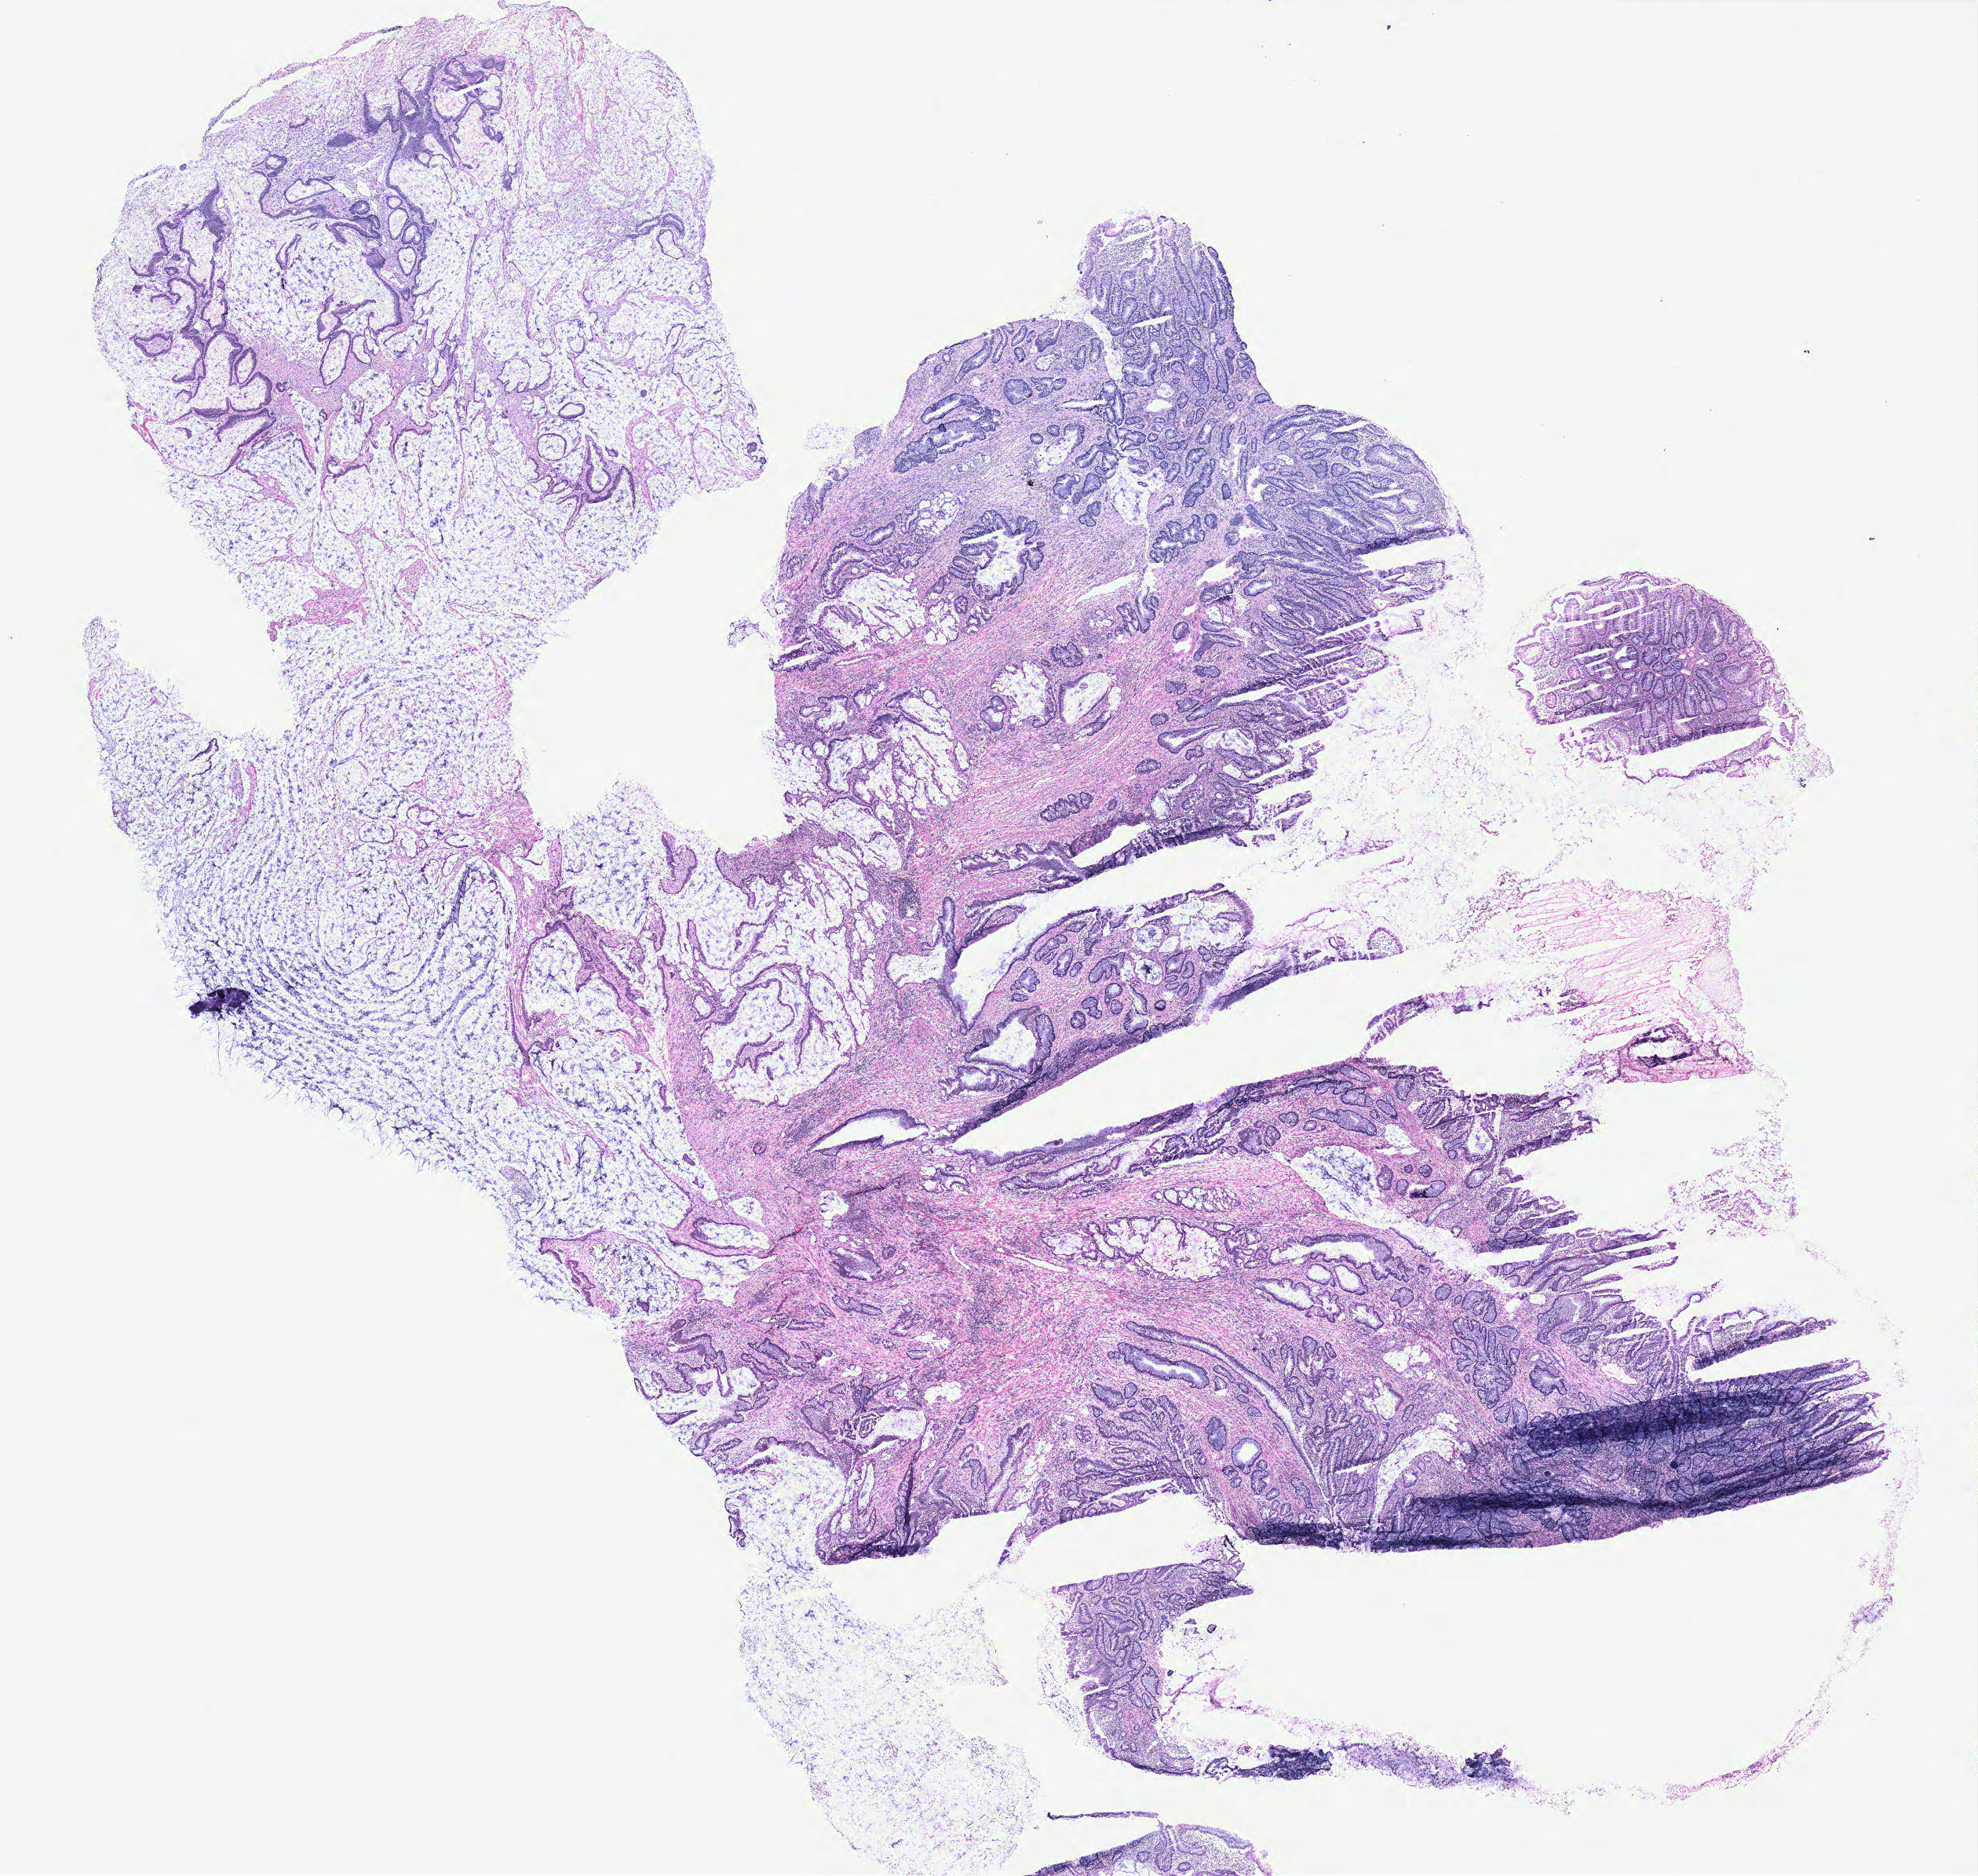
H&E-stained whole-slide image — shown as a low-resolution overview of the whole scanned area (about 20.2 x 19.1 mm, from a 40x scan). Colon, tissue type not recorded.
- patient diagnosis (cohort enrolment): colon cancer (colon)